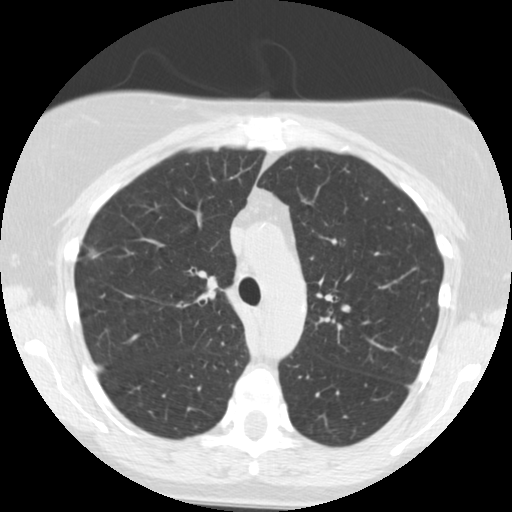
Axial slice from a low-dose chest CT screening exam; second annual screen; lung window (W 1500 / L -600 HU); 2.5 mm slice thickness; slice 166 of 244 in the series. Female participant, aged 55 years at enrolment. Current smoker at enrolment.
Expert-annotated lung lesion, bounding box <68,236,114,279> (left, top, right, bottom; pixels). Screening reader's record for this exam: no non-calcified nodule ≥4 mm recorded. Official screen result: negative screen, minor abnormalities not suspicious for lung cancer. Later outcome: lung cancer diagnosed 621 days after this screen — bronchiolo-alveolar adenocarcinoma, NOS, right upper lobe, moderately differentiated (G2), stage IIA (AJCC 6th edition), 13 mm at pathology.